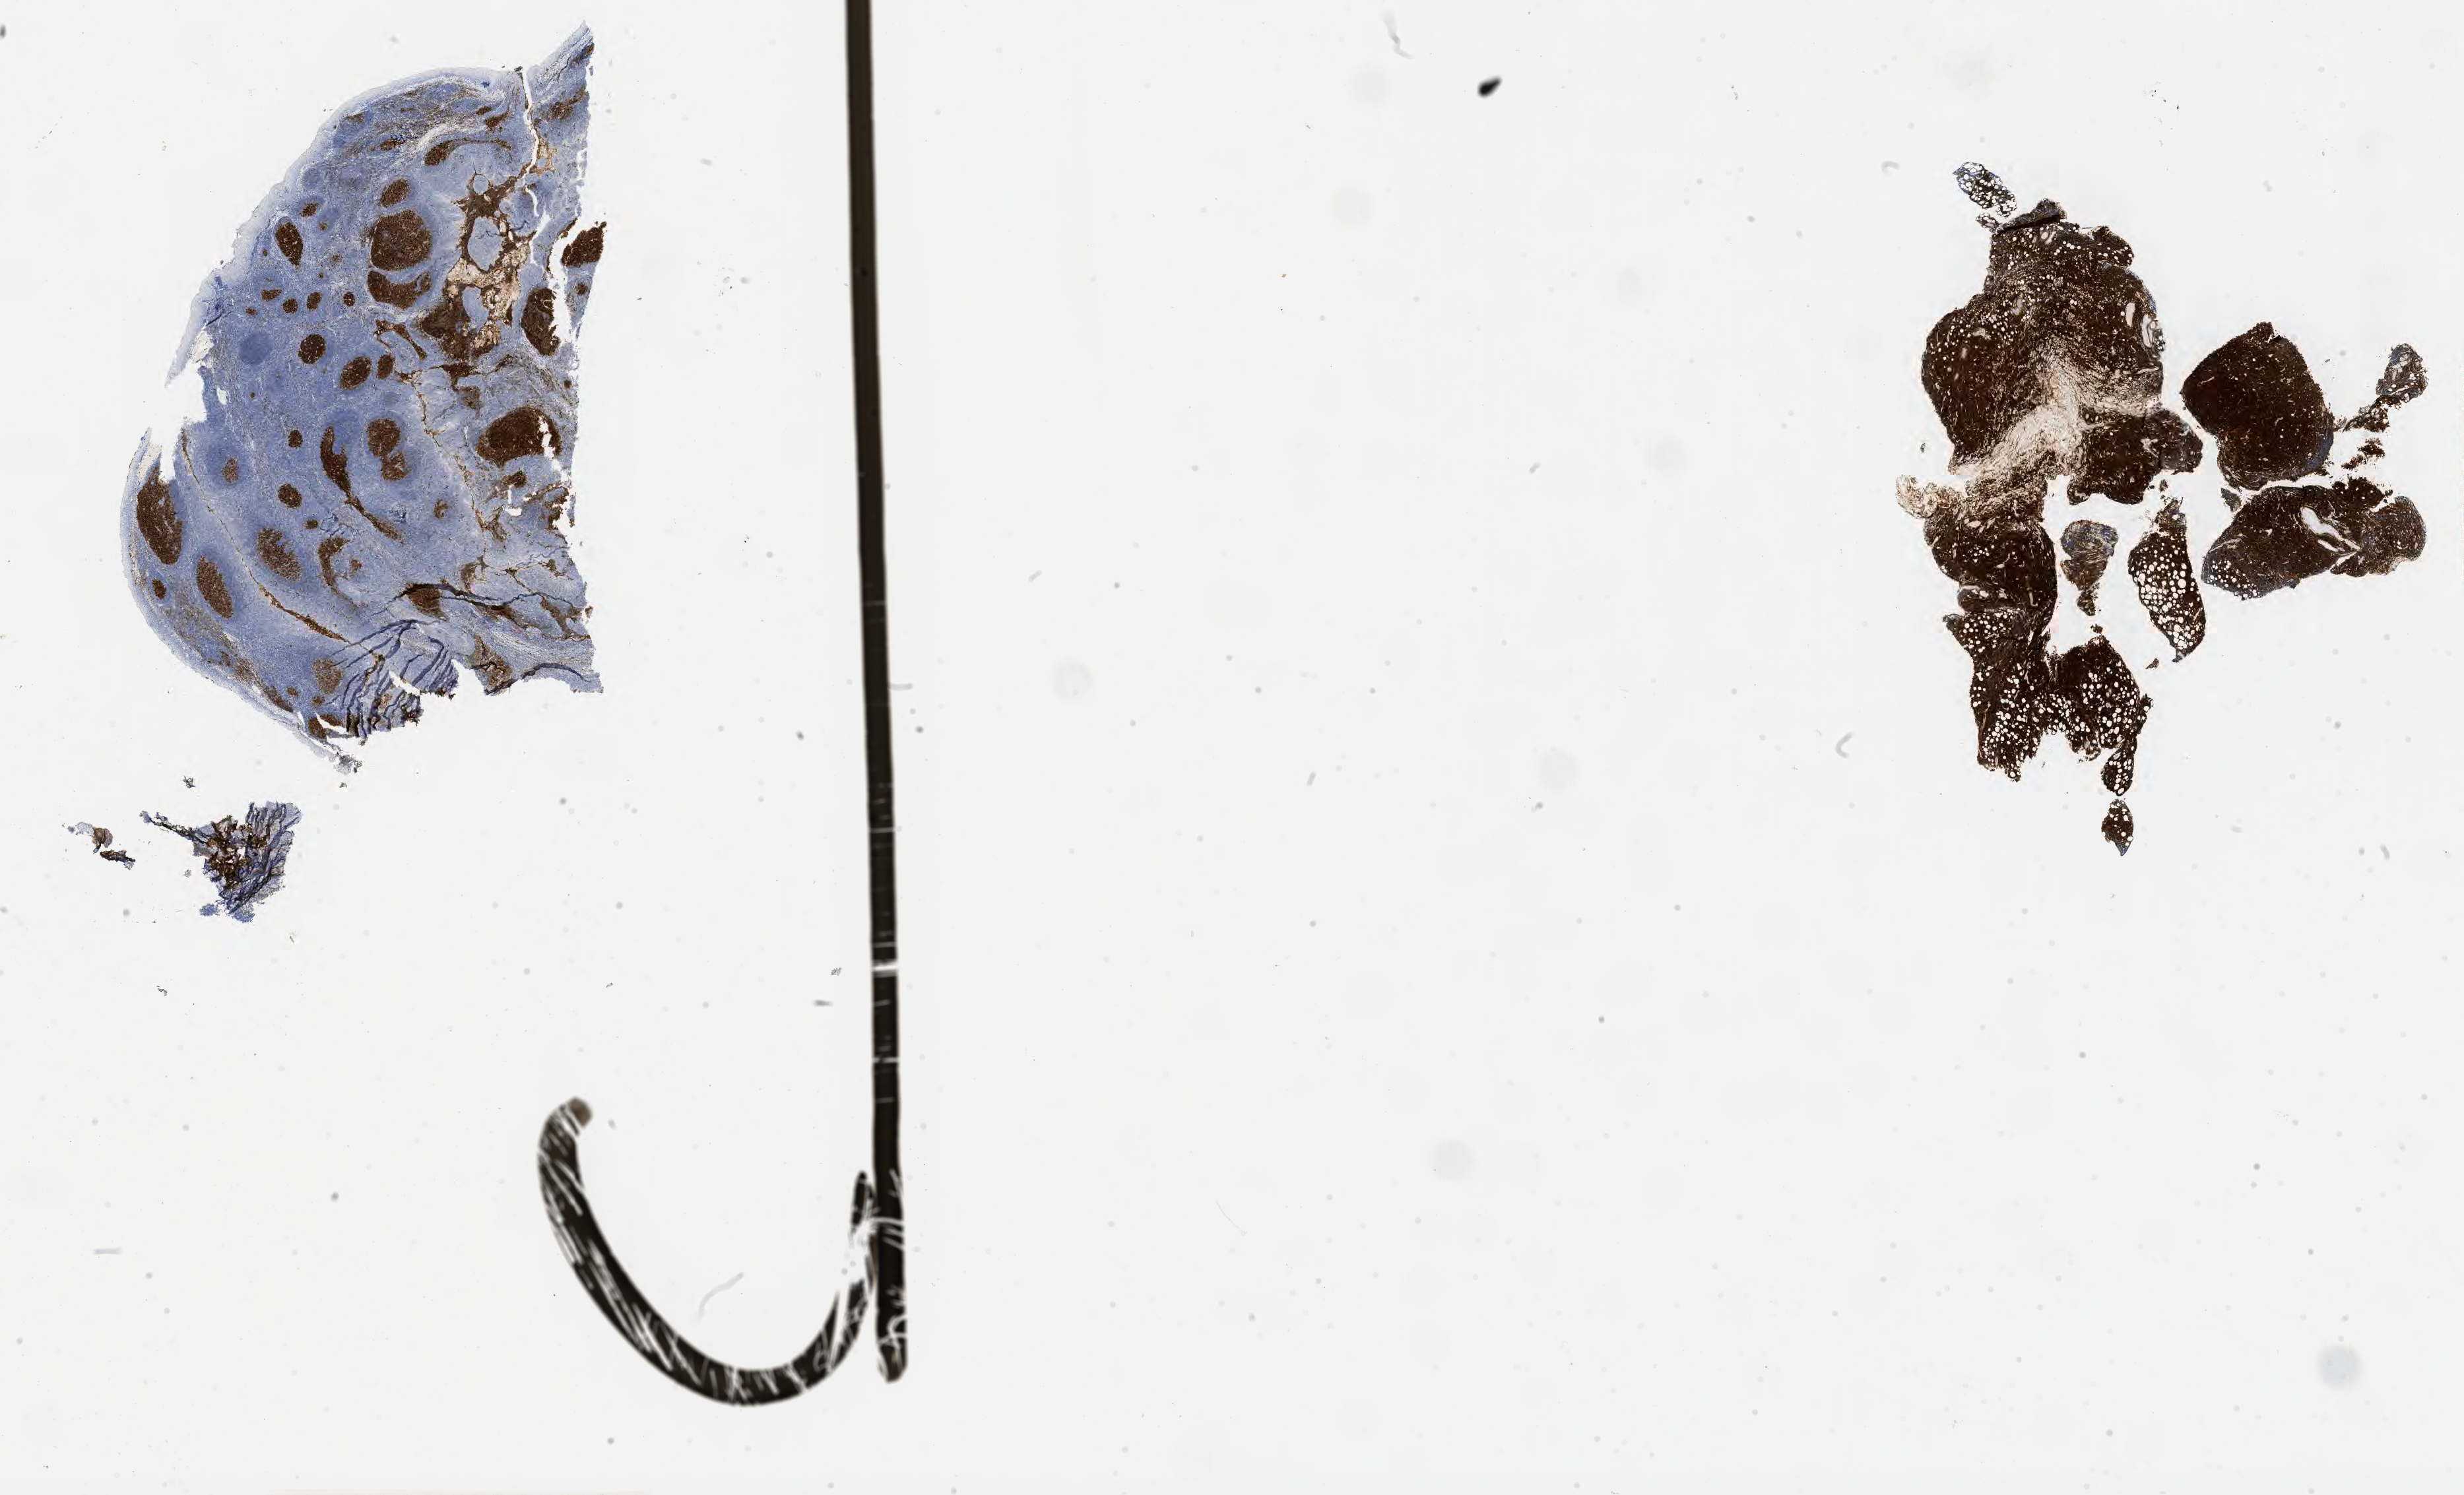
Immunohistochemistry (IHC) whole-slide image stained for CD10, low-resolution overview of the scanned area, about 30.2 x 18.3 mm; specimen: tumor tissue; anatomic site: orbit. Male patient, age 20 years.
Histologic diagnosis: Burkitt lymphoma, NOS.